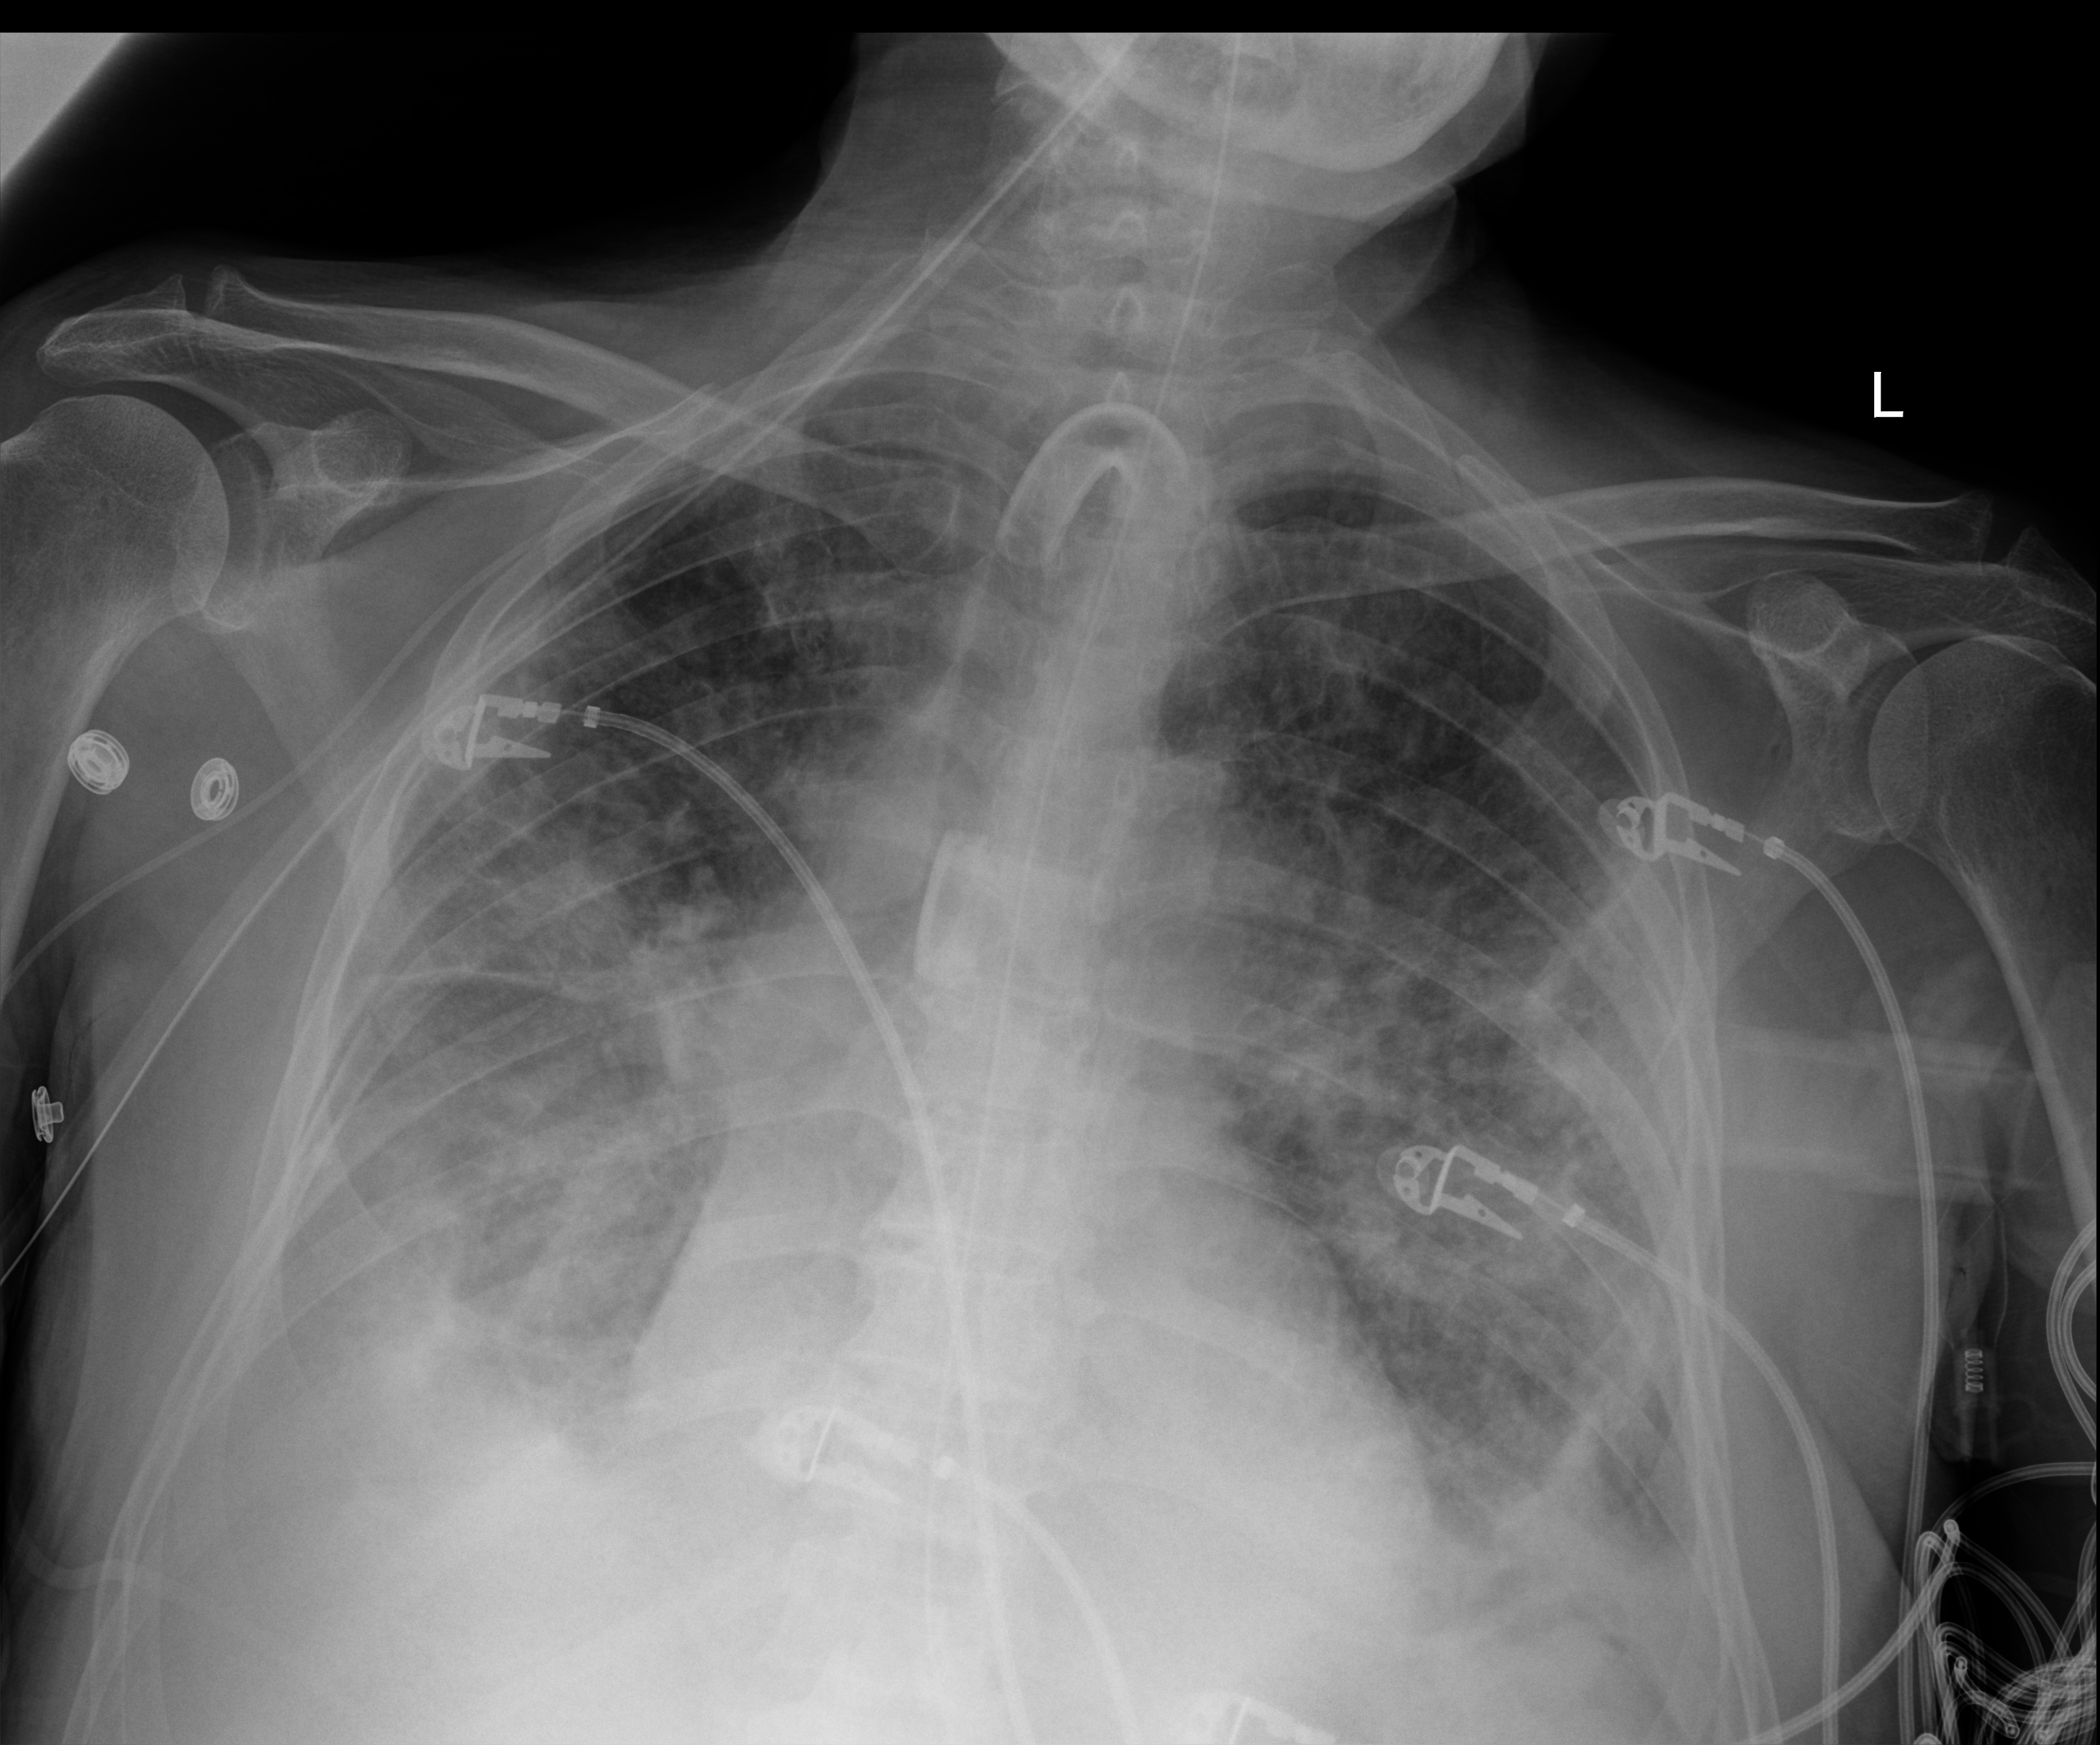
Chest X-ray (portable), anteroposterior (AP) projection. Male patient hospitalised with COVID-19, age 75–90 years.
Admission-level facts for this patient (not findings on this image; timing relative to this image not recorded): admitted to intensive care during this hospital stay: yes; mechanically ventilated during this hospital stay: yes.